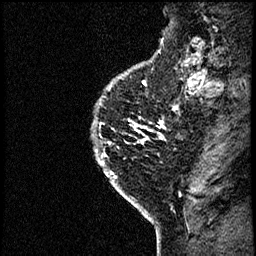
Breast MRI (dynamic contrast-enhanced), one sagittal slice. Position 54 of 60 along the scan axis. Dynamic contrast-enhanced study with each time point stored as its own series, time point 2 of 4 at this slice position (early post-contrast, ordered by acquisition time). 1.5 T. TE 4.2 ms, TR 17.6 ms. 2 mm slice thickness. 256 × 256 image matrix, field of view 200 × 200 mm. Patient: female, 40 years. From the clinical record (not read from this slice): setting: breast cancer imaged before/during neoadjuvant chemotherapy; receptor status: HER2-positive.
Outlined on this slice (semi-automatic segmentation, software-assisted and operator-edited):
- analysis volume of interest (the breast-tissue region the enhancement analysis was run in; not a lesion): bounding box [x1, y1, x2, y2] px = [86, 55, 185, 206]
- tumour enhancement mask (voxels above the 100 % enhancement threshold inside the analysis volume of interest): [95, 125, 160, 206]